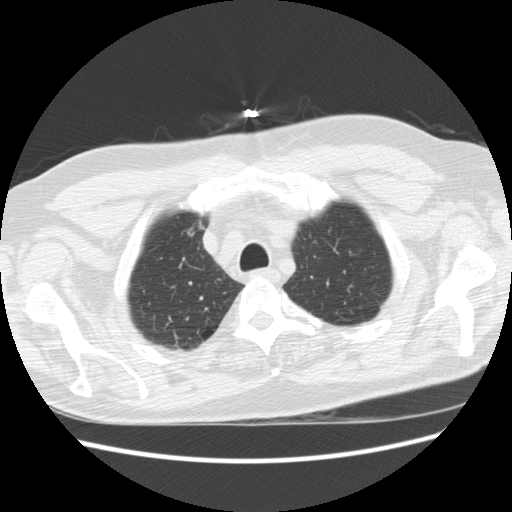
Axial slice from a low-dose chest CT screening exam; baseline screening round; lung window (W 1500 / L -600 HU); standard (soft-tissue) reconstruction kernel (STANDARD); slice 42 of 241 in the series. Male, age 66 years at enrolment. Former smoker at enrolment.
- Lesion marked by an expert reader, box from (x=174, y=212) to (x=211, y=249) px.
- Screening reader's record for this exam: no non-calcified nodule ≥4 mm recorded.
- Official screen result: negative screen, significant abnormalities not suspicious for lung cancer.
- Lung cancer was diagnosed 951 days after this screen (after the third annual screen): bronchiolo-alveolar adenocarcinoma, NOS, right upper lobe, moderately differentiated (G2), stage IA (AJCC 6th edition), 12 mm at pathology.